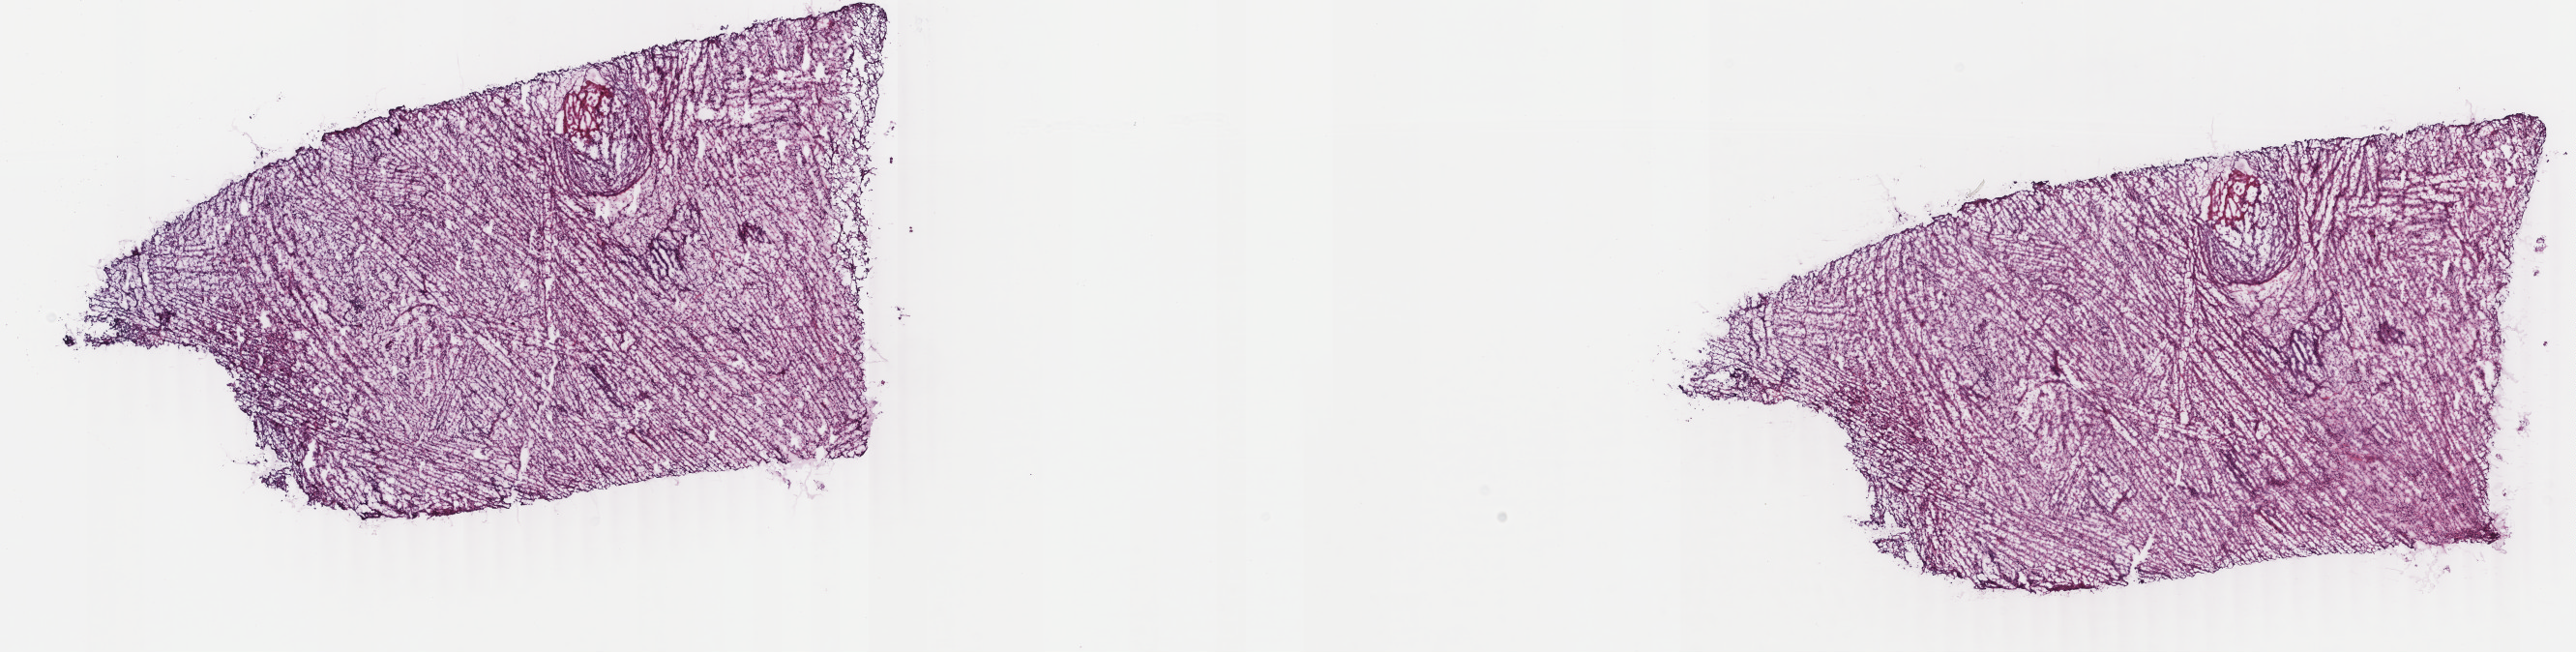
Digitized H&E-stained tissue section (whole slide) — low-resolution overview of the scanned area, about 21.2 x 5.4 mm; frozen section from the top of the tissue portion; retroperitoneum and peritoneum, primary tumour sample. Female patient; age at initial diagnosis 40 years. Pathologist review of this section (percent, as recorded): tumour cells 100%, tumour nuclei 92%, normal cells 0%, stromal cells 0%, necrosis 0%. Infiltration values recorded for this section: lymphocyte infiltration 0%, monocyte infiltration 0%, neutrophil infiltration 0%.
Pathologic diagnosis: Dedifferentiated liposarcoma (retroperitoneum).